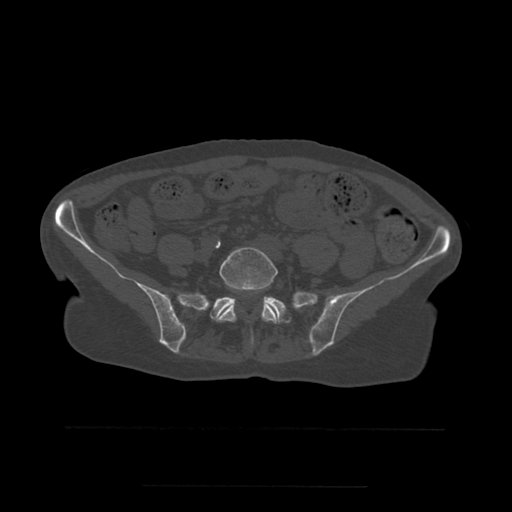
CT including the spine, one axial slice; slice 138 of 544 in the series (ordered by position); bone window (W 1800 / L 400 HU); 1.25 mm slice thickness; 512 × 512 image matrix, field of view 350 × 350 mm. Patient age 58 years. From the clinical record (not read from this slice): primary cancer: lung.
Outlined on this slice (semi-automatic segmentation, software-assisted and operator-edited):
- L5 vertebra: bounding box (x1, y1, x2, y2) in pixels: (217, 247, 279, 345)